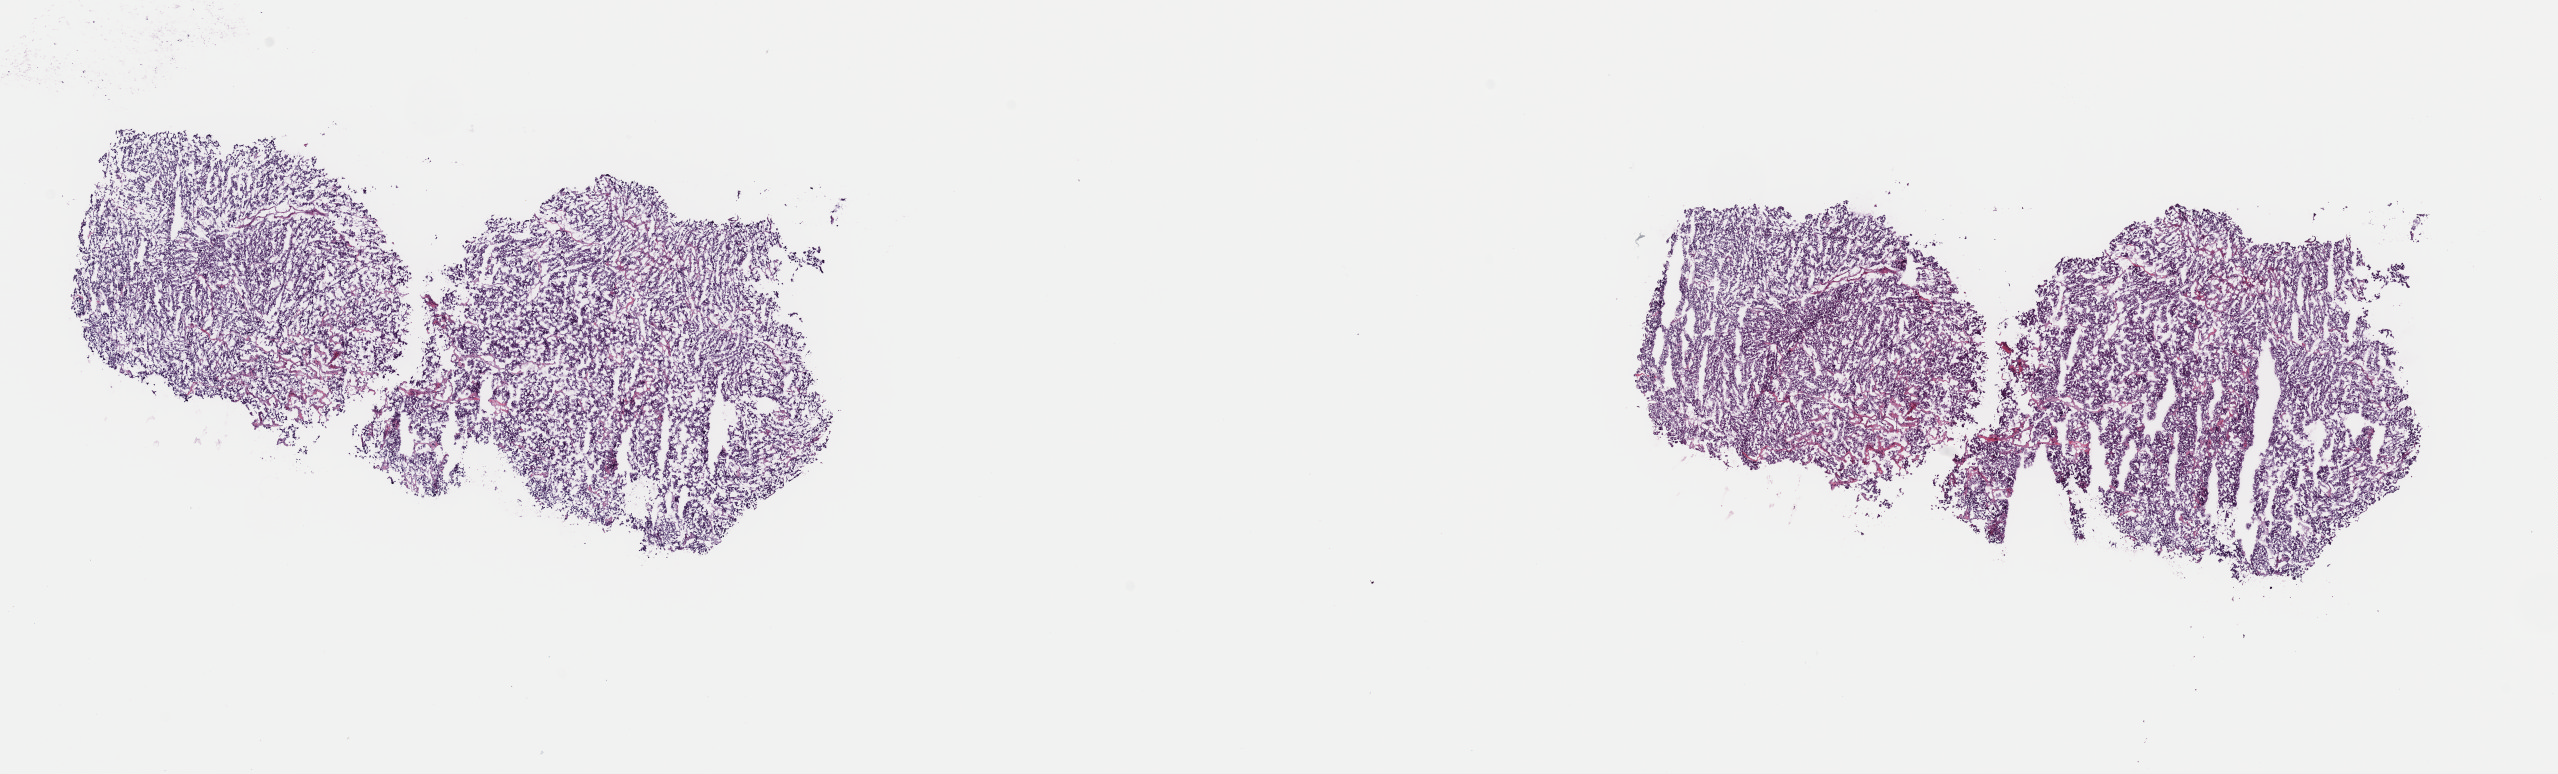
Digitized H&E tissue section (whole slide), whole scanned area (about 20.2 x 6.1 mm, acquisition: 40x scan) shown as a low-resolution overview; frozen section from the top of the tissue portion; adrenal gland, primary tumour sample. Female, age 35 years at initial diagnosis. Slide review estimates, as recorded: tumour cells 90%, tumour nuclei 100%, normal cells 0%, stromal cells 10%, necrosis 0%. Infiltration values recorded for this section: lymphocyte infiltration 0%, monocyte infiltration 0%, neutrophil infiltration 0%.
* pathologic diagnosis: Pheochromocytoma, NOS
* laterality: left